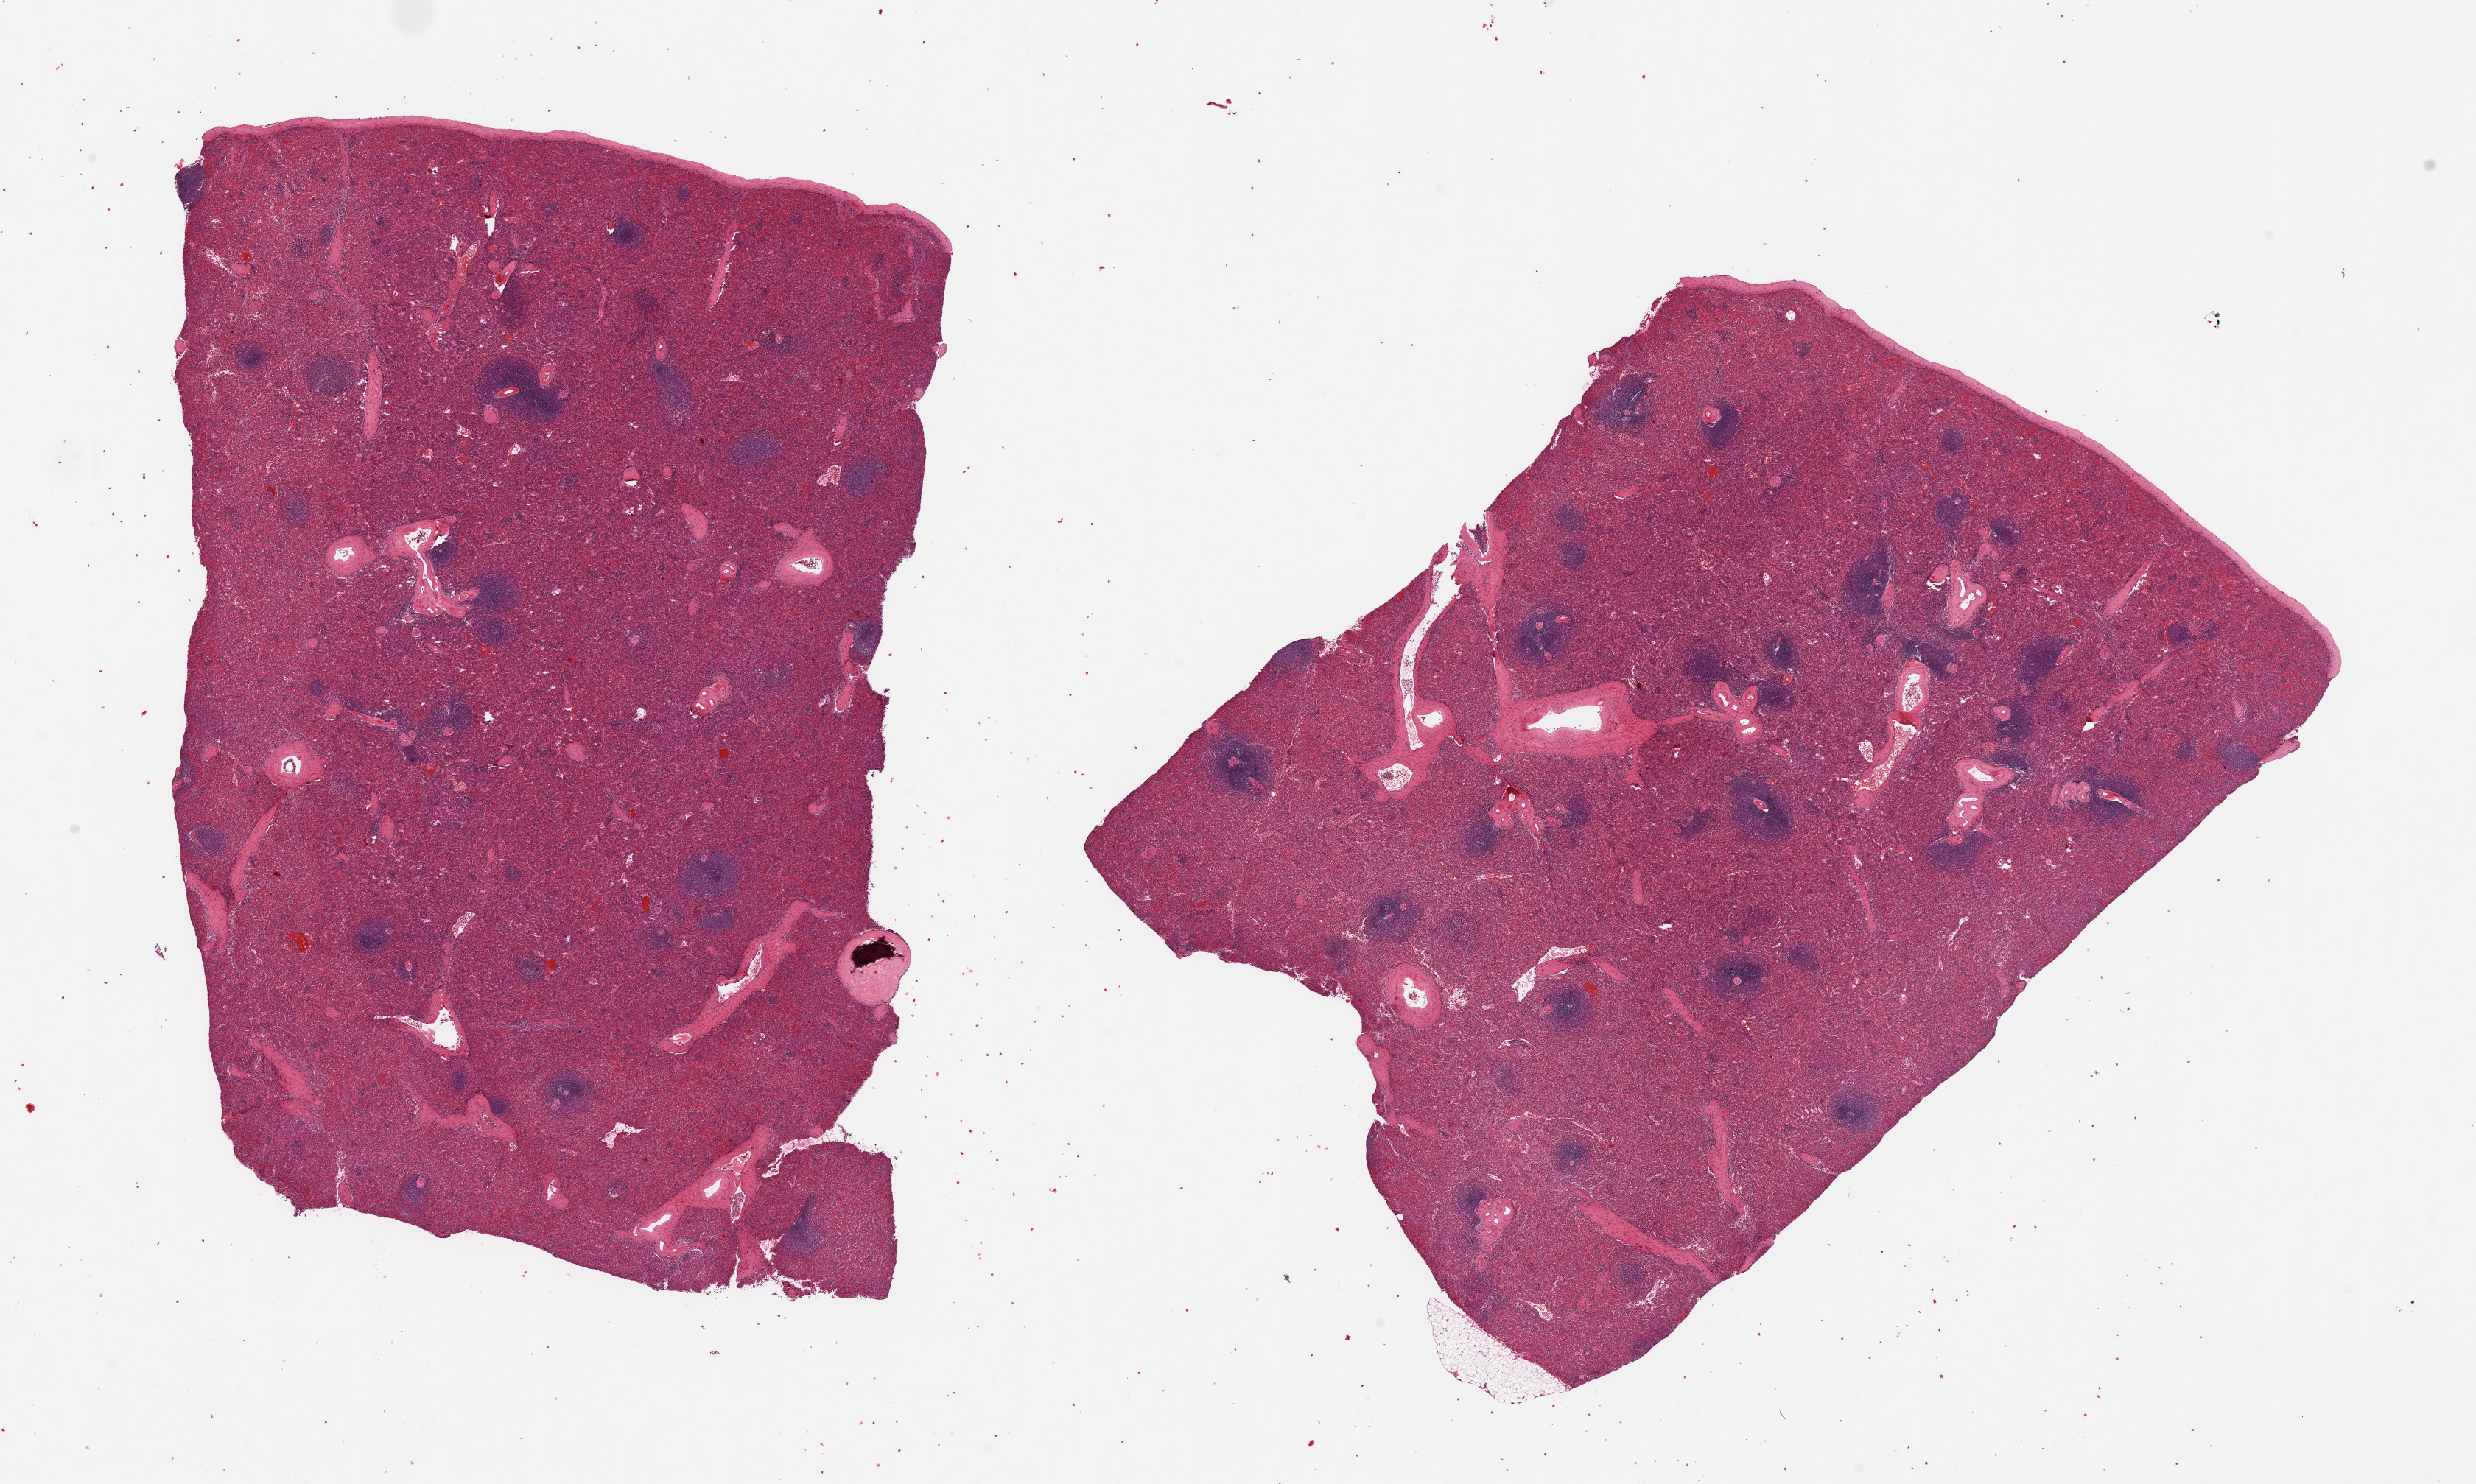
H&E whole-slide image — low-resolution overview of the scanned area, about 26.6 x 15.9 mm (slide scanned at 20x); PAXgene-fixed, paraffin-embedded tissue; target tissue: spleen; tissue donor sample. Donor sex: female.
* reviewer comment on this tissue sample: 2 pieces, mild congestion, includes capsule (target is 5 mm below capsule)